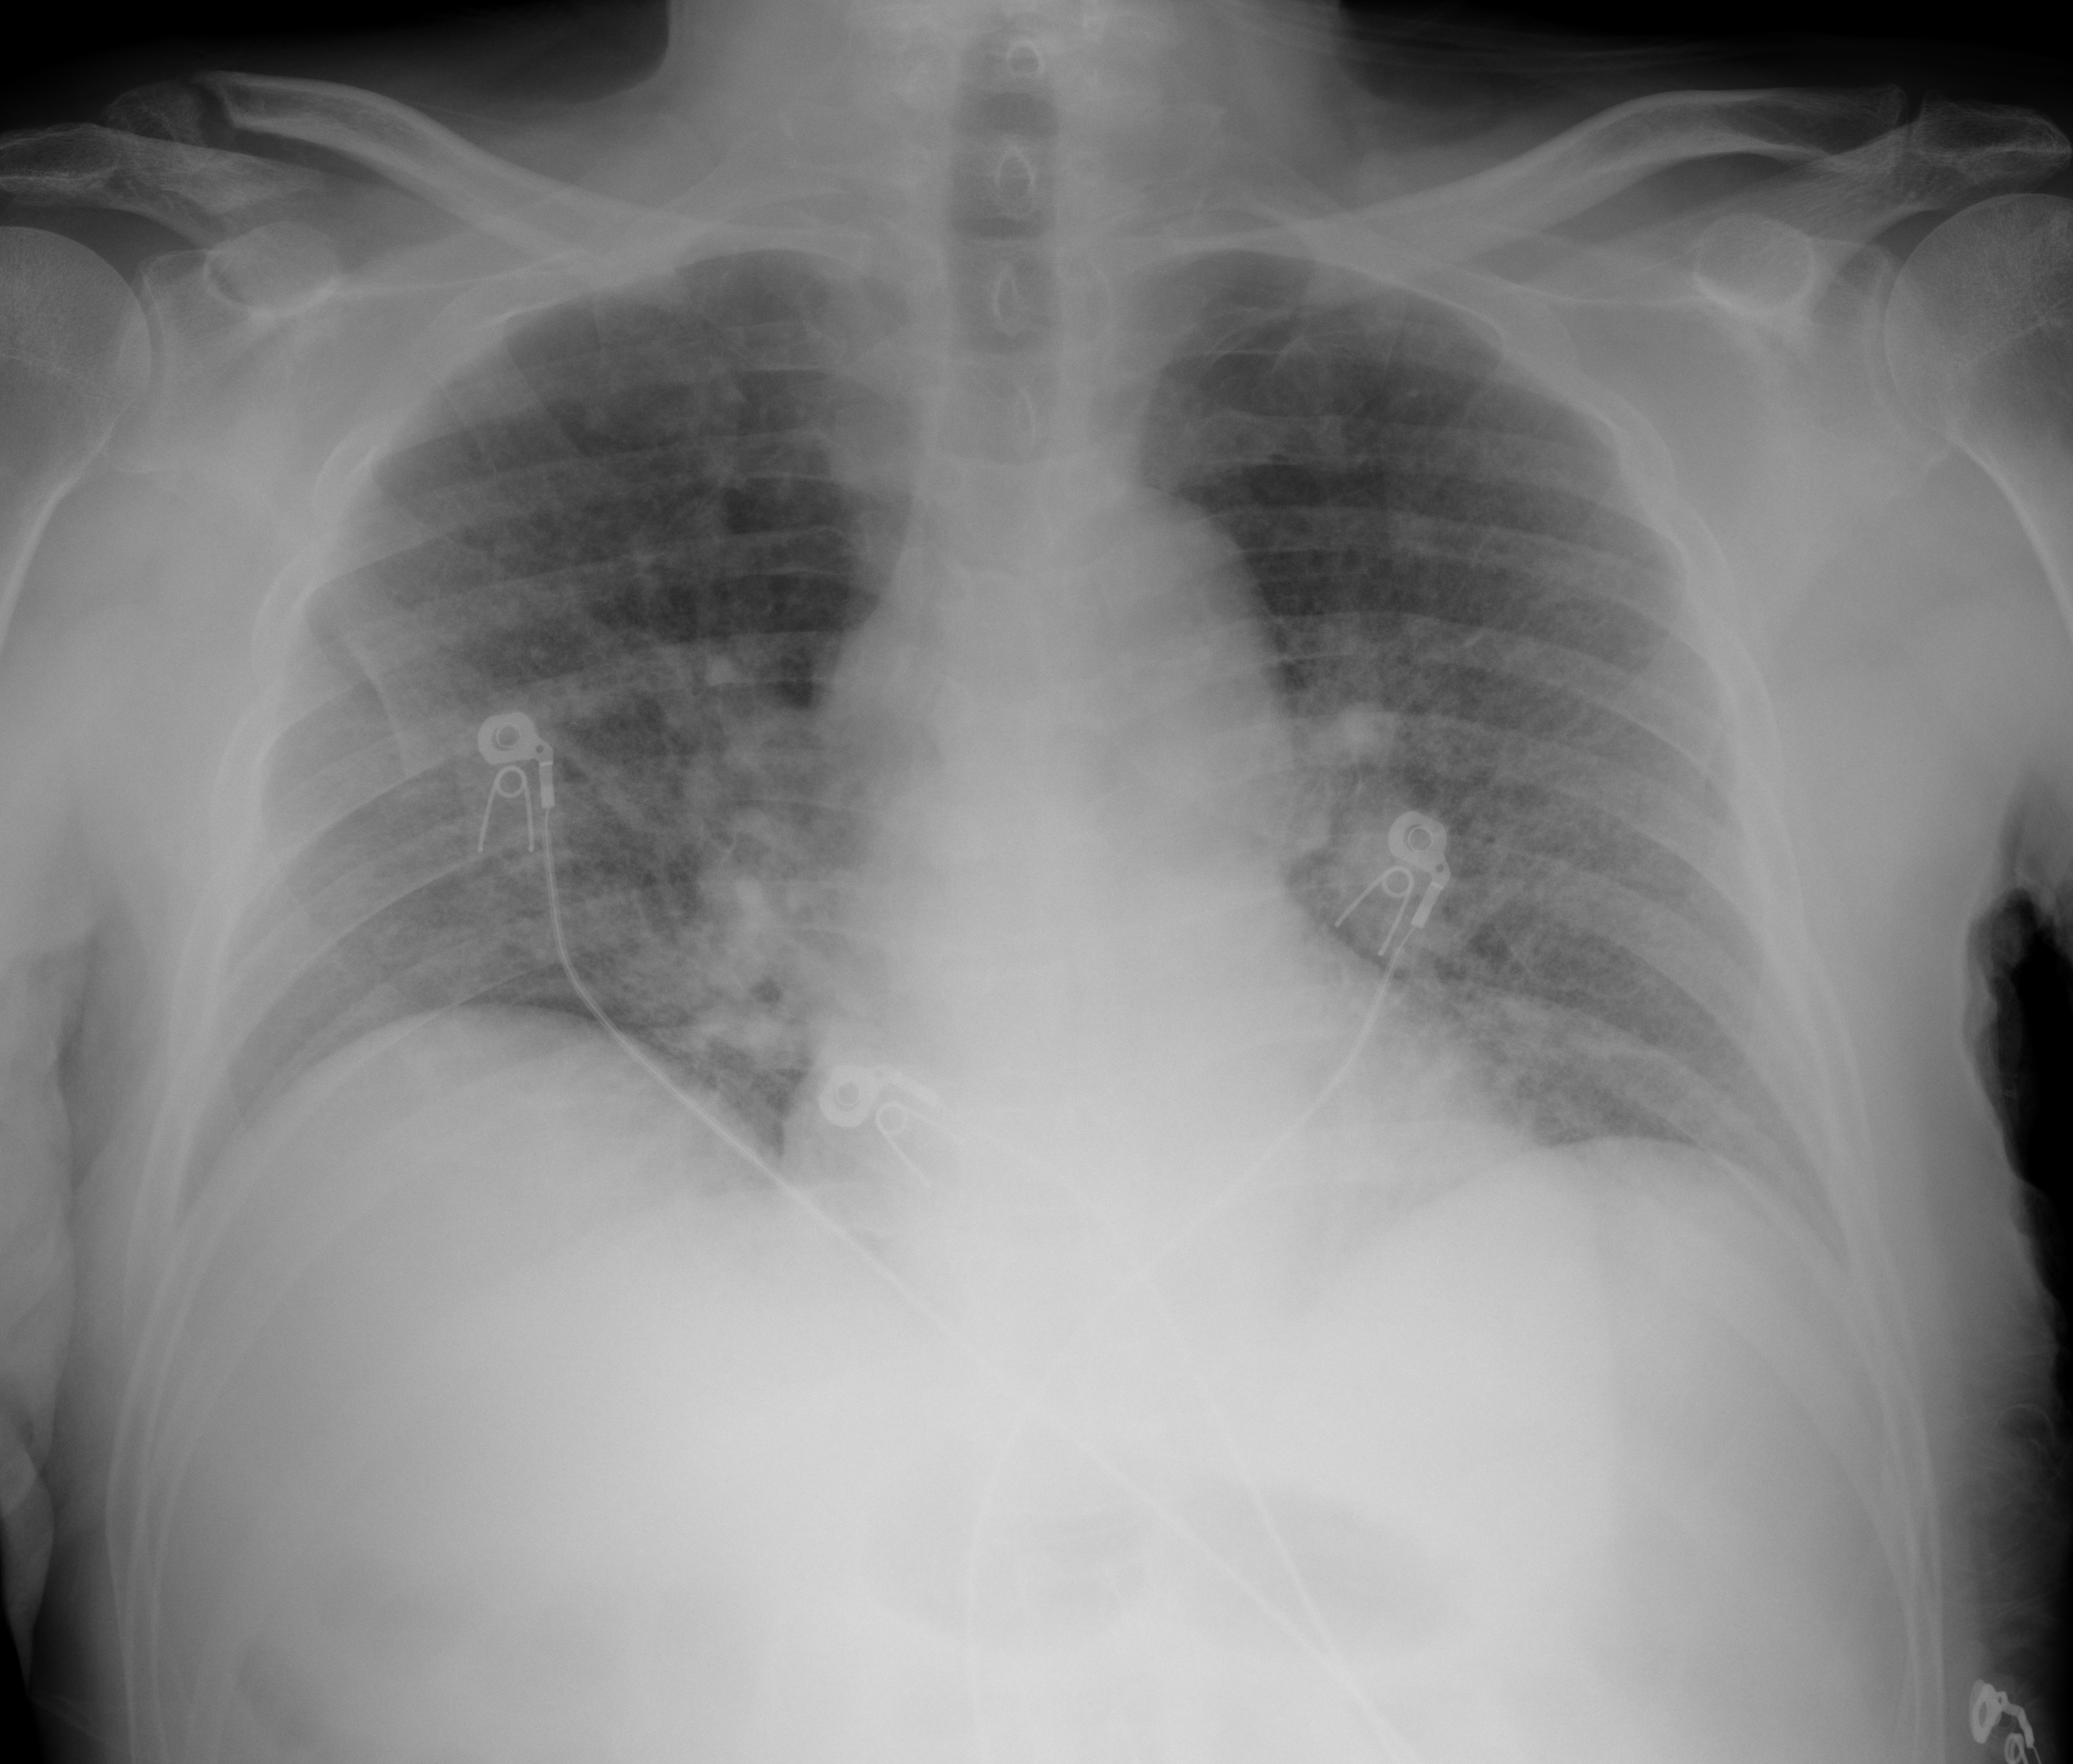
Portable chest radiograph, AP projection. Male patient, age 70 years; imaged 0 days after the COVID-19 diagnosis.
Radiologist's key findings for this exam: There is mild, diffuse interstitial reticular pattern throughout the lungs.